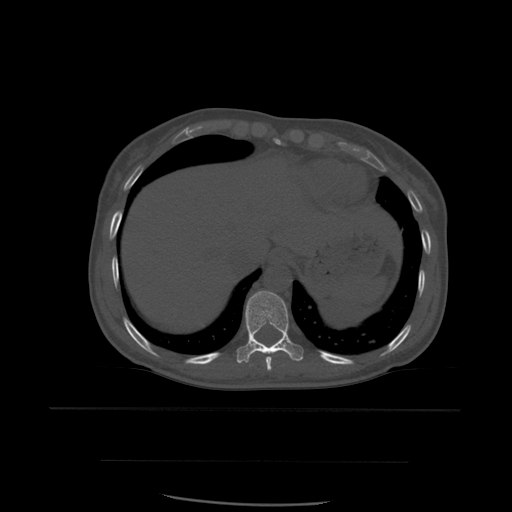
CT including the spine, one axial slice; position 319 of 574 along the scan axis; bone window (W 1800 / L 400 HU); 1.25 mm slice thickness; 512 × 512 image matrix, field of view 392 × 392 mm. Patient age 48 years. From the clinical record (not read from this slice): primary cancer: lung.
Outlined on this slice (semi-automatically segmented with operator editing):
- T10 vertebra: bounding box [x1, y1, x2, y2] px = [237, 291, 304, 364]
- T9 vertebra: [266, 345, 282, 371]